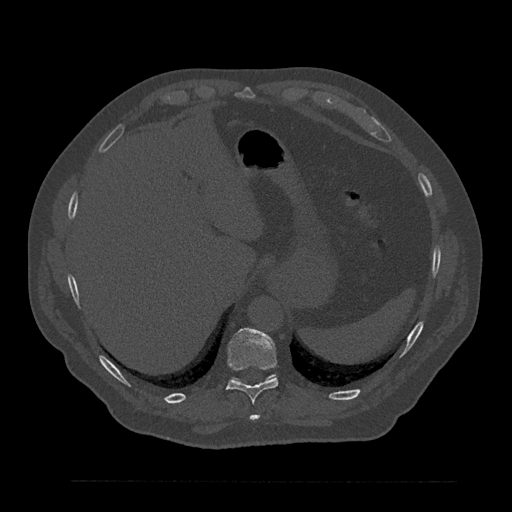
CT including the spine, one axial slice; position 339 of 797 along the scan axis; reconstruction kernel Br40s/3; 120 kVp; bone window (W 1800 / L 400 HU); 512 × 512 image matrix, field of view 430 × 430 mm. Male patient, age 61 years. Case-level facts recorded for this patient, not image findings: primary cancer: prostate.
Outlined on this slice (semi-automatically segmented with operator editing):
- T10 vertebra: bounding box <227,328,278,404> (left, top, right, bottom; pixels)
- T11 vertebra: <232,375,274,381>
- T9 vertebra: <249,415,259,421>